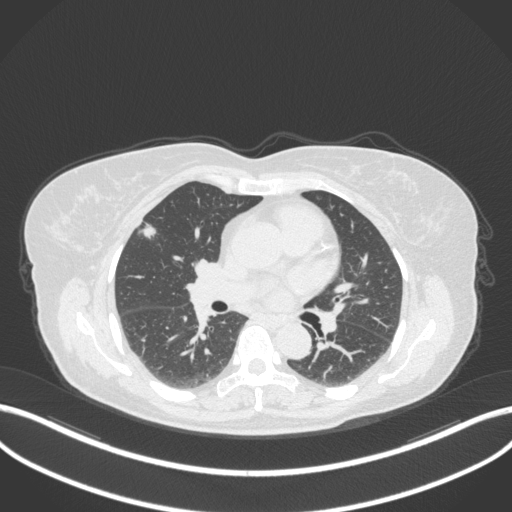
Chest CT, one axial slice; position 183 of 310 along the scan axis; reconstruction kernel B31f; lung window (W 1500 / L -600 HU); 512 × 512 image matrix, field of view 400 × 400 mm. Female patient, age 55 years. From the clinical record (not read from this slice): clinical TNM (as recorded): T1b N0 M0.
Annotated regions visible in this slice (rectangle marked by the reading radiologist):
- lung tumour (recorded histology: adenocarcinoma): bounding box (x1, y1, x2, y2) in pixels: (136, 218, 161, 241)